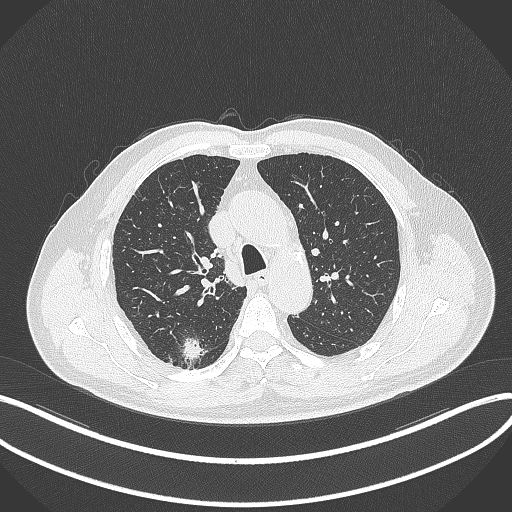
Chest CT, one axial slice. Slice 263 of 359 in the series (ordered by position). Reconstruction kernel B70f. 120 kVp. Lung window (W 1500 / L -600 HU). 512 × 512 image matrix, field of view 400 × 400 mm. Male patient, age 69 years. From the clinical record (not read from this slice): clinical TNM (as recorded): T1b N0 M0.
Structures marked on this image (rectangle marked by the reading radiologist):
- lung tumour (recorded histology: adenocarcinoma): box from (x=181, y=329) to (x=204, y=363) px